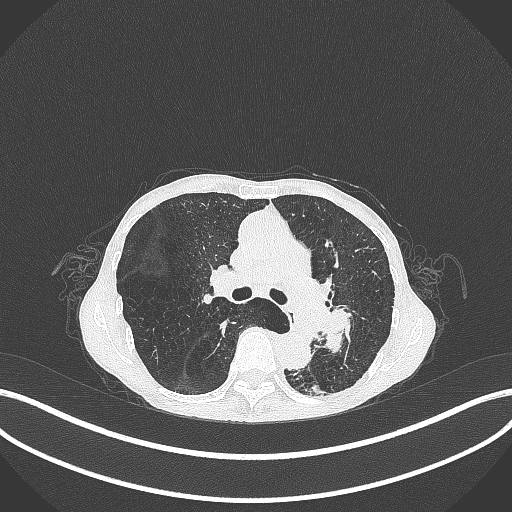
Chest CT, one axial slice. Position 172 of 347 along the scan axis. Reconstruction kernel B70f. 120 kVp. Lung window (W 1500 / L -600 HU). 512 × 512 image matrix. Female patient, age 70 years. Case-level facts recorded for this patient, not image findings: clinical TNM (as recorded): T3 N0 M0.
Structures marked on this image (rectangle marked by the reading radiologist):
- lung tumour (recorded histology: small cell carcinoma): bounding box (x1, y1, x2, y2) in pixels: (325, 299, 357, 358)